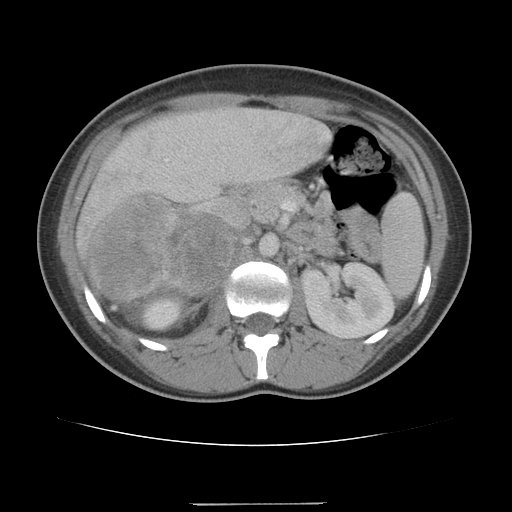
Contrast-enhanced abdominal CT, one axial slice. Reconstruction kernel STANDARD. 120 kVp. Soft-tissue window (W 400 / L 40 HU). 5 mm slice thickness. 512 × 512 image matrix, field of view 360 × 360 mm. Female patient, age 21 years. From the clinical record (not read from this slice): diagnosis: adrenocortical carcinoma; tumour side: right adrenal; tumour size at pathology: 15.5 cm; Ki-67 index: 26 %; stage (as recorded): 3.
Outlined on this slice (semi-automatically segmented with operator editing):
- mass: bounding box (x1, y1, x2, y2) in pixels: (90, 200, 235, 301)